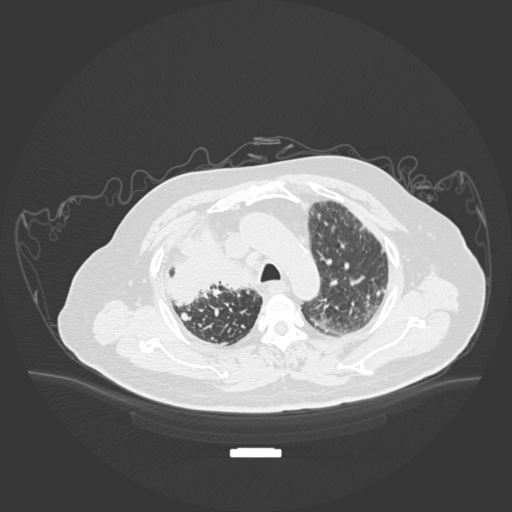
Chest CT, one axial slice; slice 140 of 201 in the series (ordered by position); reconstruction kernel B30f; lung window (W 1500 / L -600 HU); 512 × 512 image matrix, field of view 500 × 500 mm. Patient: male, 69 years. From the clinical record (not read from this slice): clinical TNM (as recorded): T4 N3 M1.
Structures marked on this image (bounding box drawn by a radiologist):
- lung tumour (recorded histology: adenocarcinoma): bounding box [x1, y1, x2, y2] px = [163, 225, 258, 305]